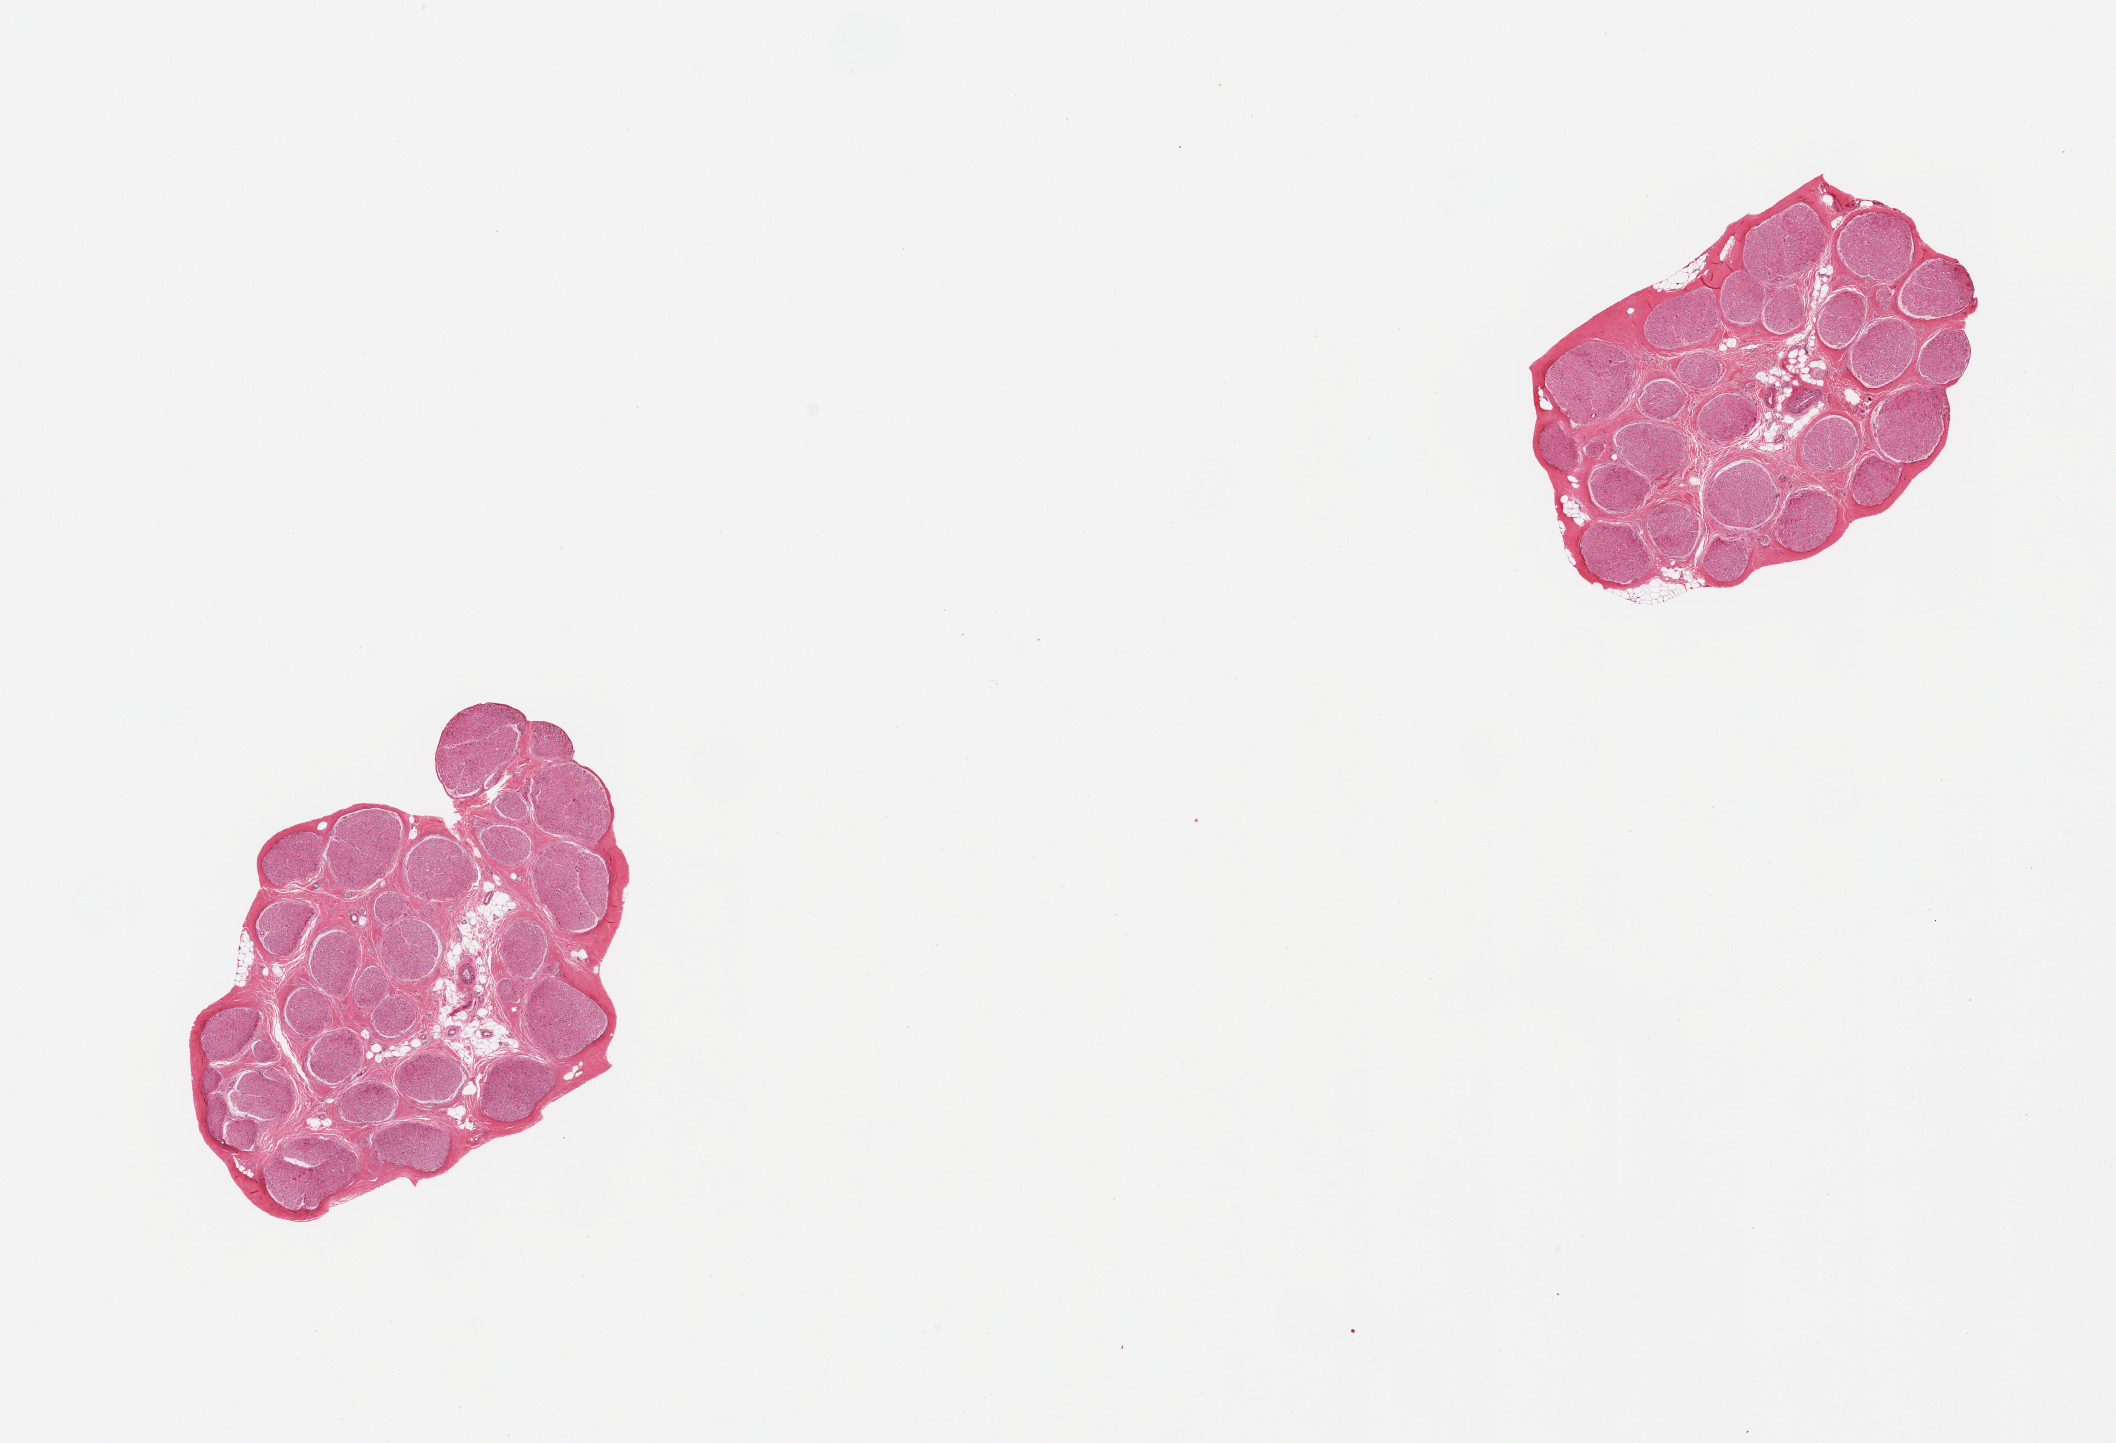
Whole-slide image, H&E stain — low-resolution overview of the scanned area, about 16.7 x 11.4 mm (slide scanned at 20x). PAXgene-fixed paraffin-embedded (PFPE) section. Target tissue: tibial nerve. Donor tissue sample. Male donor.
Pathologist's review note for this sample: 2 pieces; well trimmed; 5-10% internal fat.